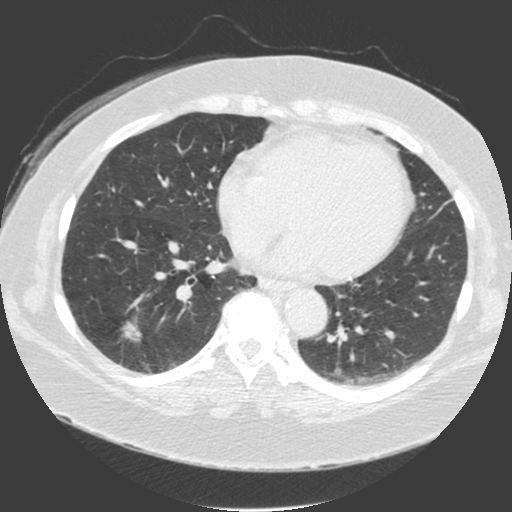
Chest CT (low-dose screening protocol), one axial image; third screening round (two years after baseline); lung window (W 1500 / L -600 HU); standard (soft-tissue) reconstruction kernel (C); slice 104 of 175 in the series; 512 × 512 image matrix. Female participant, aged 56 years at enrolment. Current smoker at enrolment.
Lesion marked by an expert reader, bounding box [x1, y1, x2, y2] px = [97, 300, 155, 357]. The screening reader recorded 4 non-calcified nodules or masses ≥4 mm on this exam; which of them this box marks is not recorded. Official screen result: positive, other. Lung cancer was diagnosed 20 days after this screen: adenosquamous carcinoma, right lower lobe, poorly differentiated (G3), stage IA (AJCC 6th edition), 25 mm at pathology.